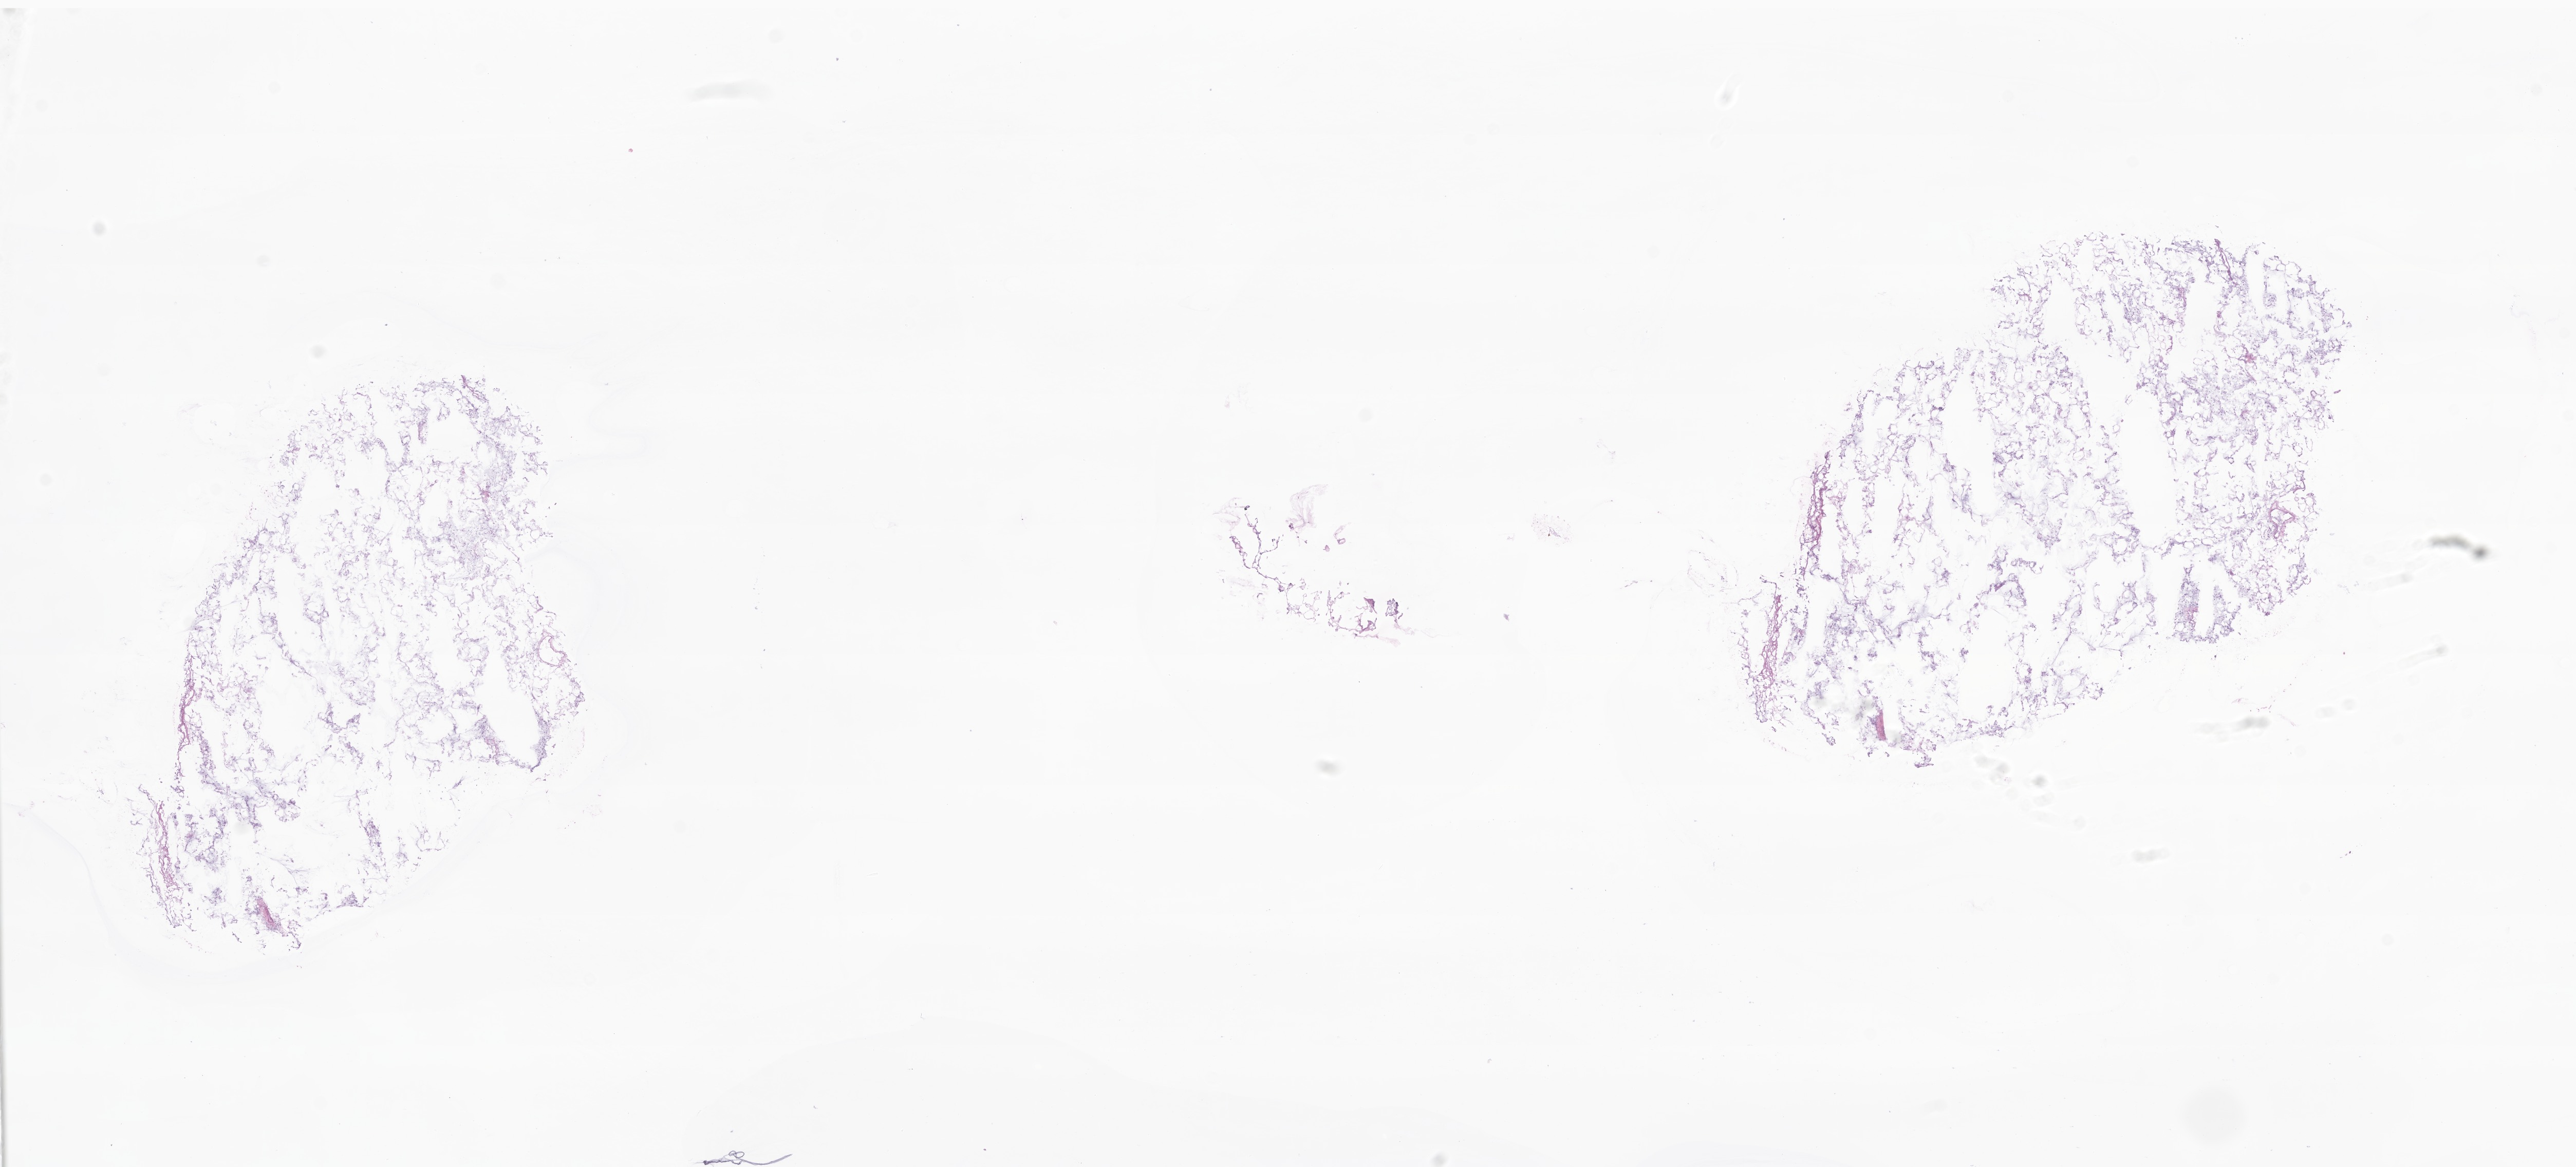
Digitized hematoxylin and eosin (H&E)-stained section of tumor tissue from the soft tissue of lower extremity — whole scanned area (about 21.1 x 9.6 mm) shown as a low-resolution overview; frozen section (OCT-embedded). Patient female; age 230 months (19 years 2 months).
• diagnosis (ICD-O-3 morphology term): Myxoid liposarcoma
• tissue or organ of origin (case record): connective, subcutaneous and other soft tissues of lower limb and hip